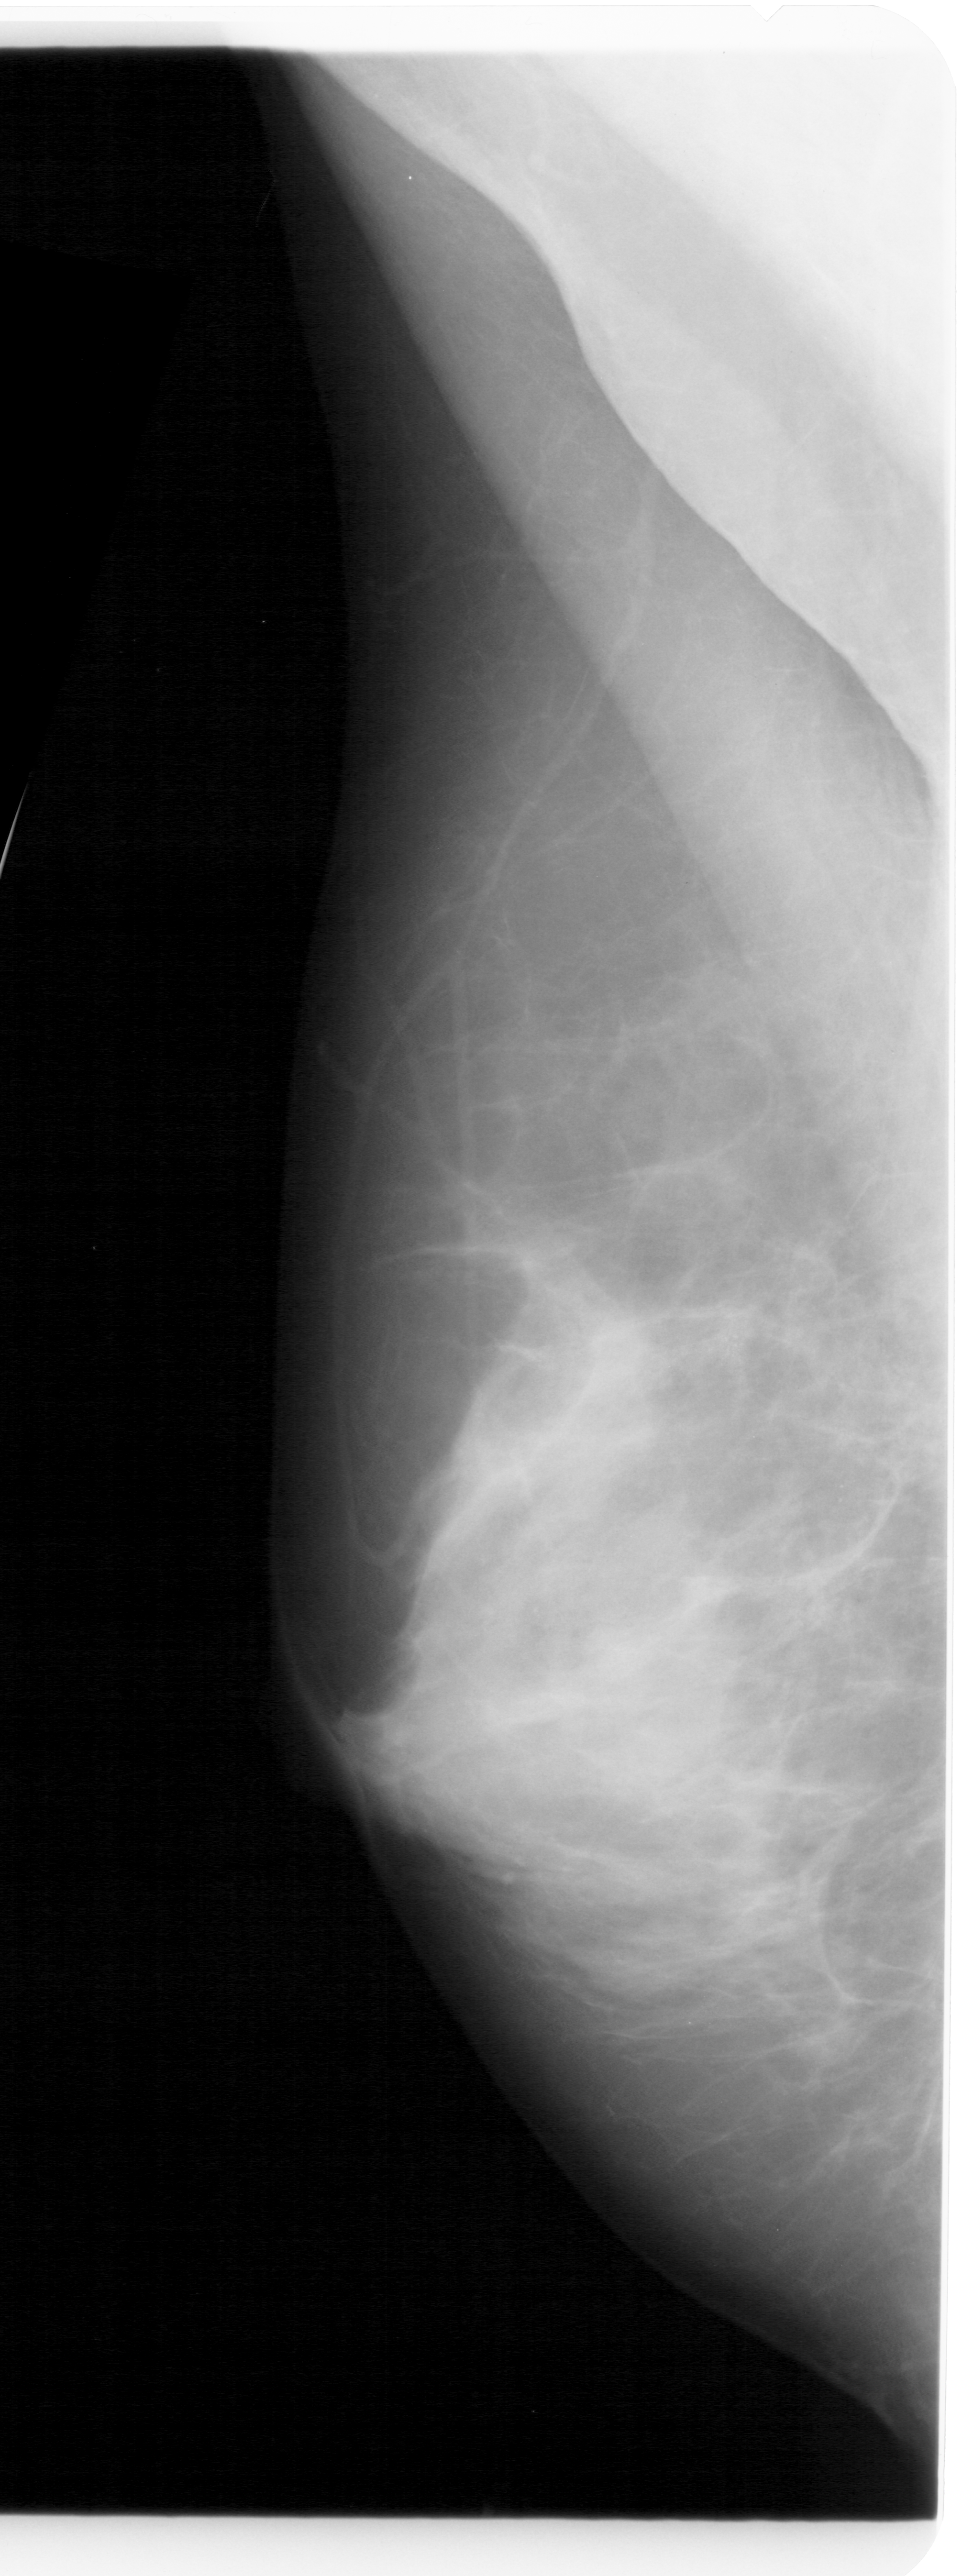
Mammogram (digitized film); left breast; mediolateral oblique (MLO) view; BI-RADS breast density category 4 (scale 1–4).
Abnormality record for this image: calcifications, morphology pleomorphic, distribution clustered; BI-RADS assessment category 4; subtlety rating 1 on a 1 (subtle) to 5 (obvious) scale; pathology result (as recorded, not read from the image): malignant.